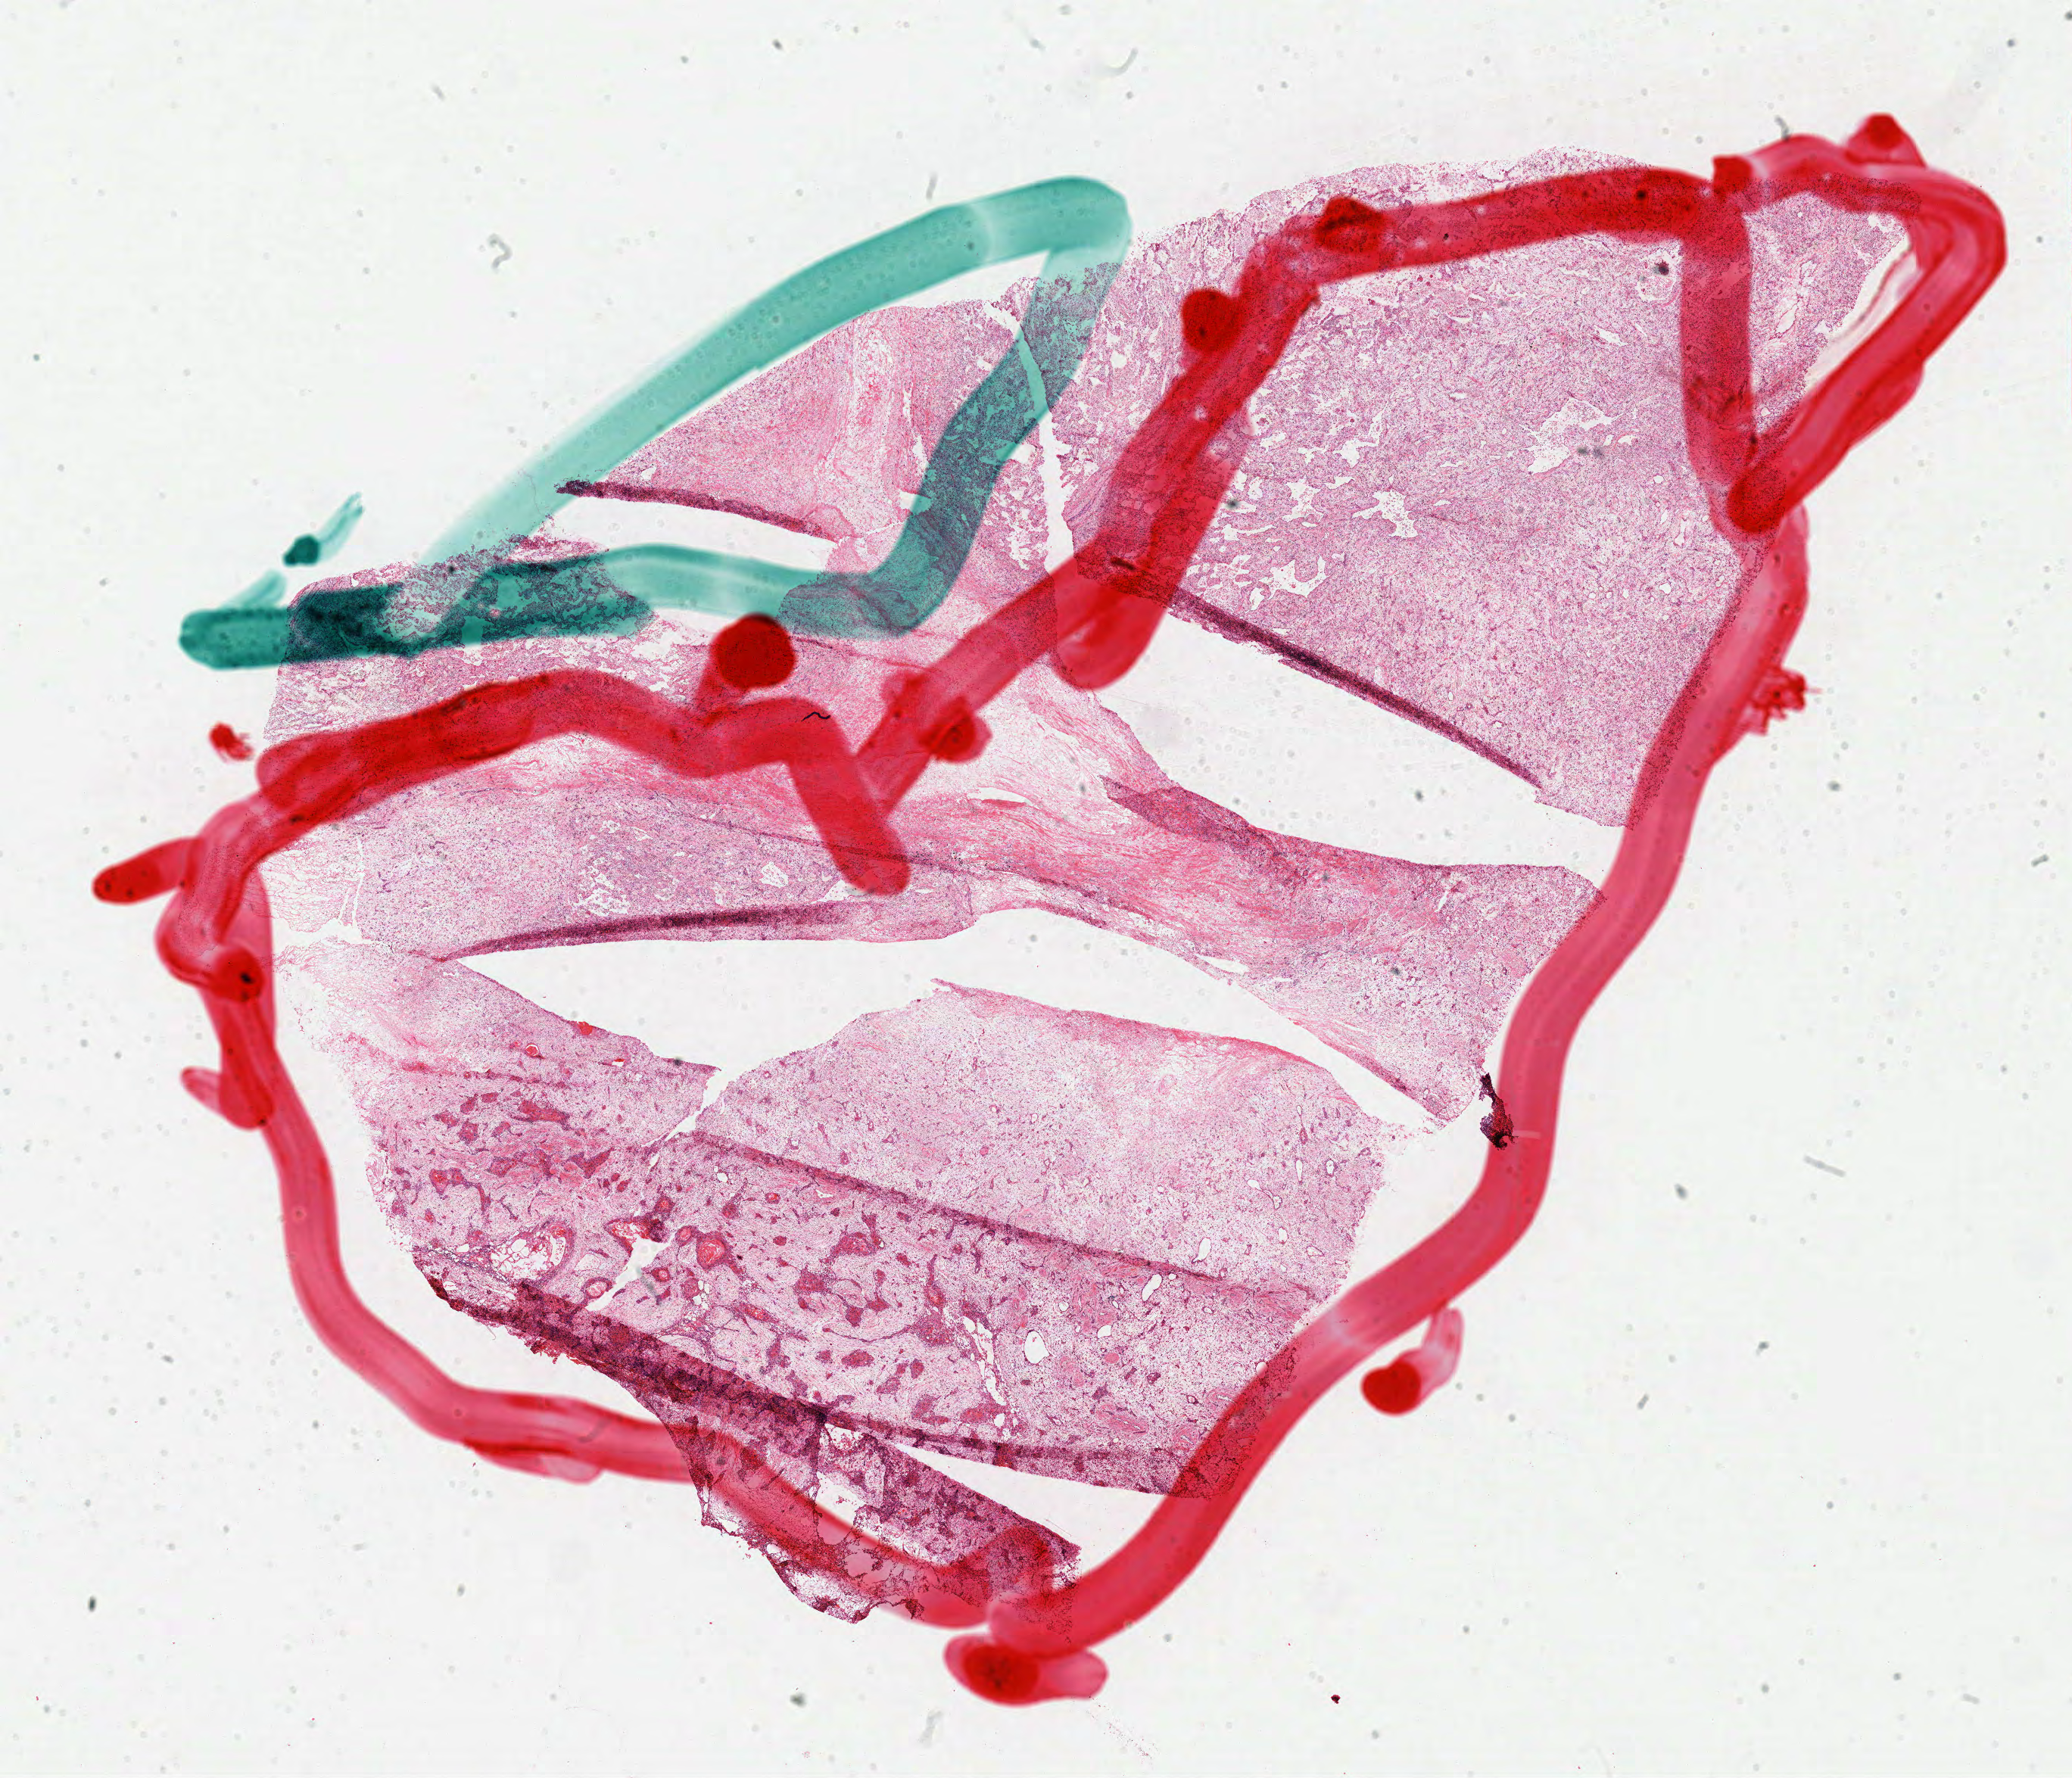
Hematoxylin and eosin (H&E) stained whole-slide image — shown as a low-resolution overview of the whole scanned area (about 21.6 x 18.5 mm, from a 40x scan); frozen section; lung, primary tumour sample. Female, age 63 years at initial diagnosis. Composition of this section per pathologist review: tumour cells 54%, tumour nuclei 70%, normal cells 15%, stromal cells 30%, necrosis 1%.
* AJCC pathologic stage: IIB (7th edition)
* laterality: left
* histologic diagnosis: Squamous cell carcinoma, NOS (upper lobe, lung)